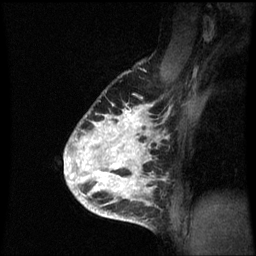
Breast MRI (dynamic contrast-enhanced), one sagittal slice. Slice 47 of 60 in the series (ordered by position). Dynamic contrast-enhanced series, image 2 of 3 at this slice position (ordered by acquisition). 1.5 T. TE 4.2 ms, TR 8.9 ms. 2 mm slice thickness. 256 × 256 image matrix. Female patient, age 35 years. Case-level facts recorded for this patient, not image findings: setting: breast cancer imaged before/during neoadjuvant chemotherapy; receptor status: HR-positive, HER2-negative.
Annotated regions visible in this slice (semi-automatically segmented with operator editing):
- analysis volume of interest (the breast-tissue region the enhancement analysis was run in; not a lesion): bounding box [x1, y1, x2, y2] px = [66, 104, 166, 215]
- tumour enhancement mask (voxels above the 70 % enhancement threshold inside the analysis volume of interest): [66, 104, 158, 215]